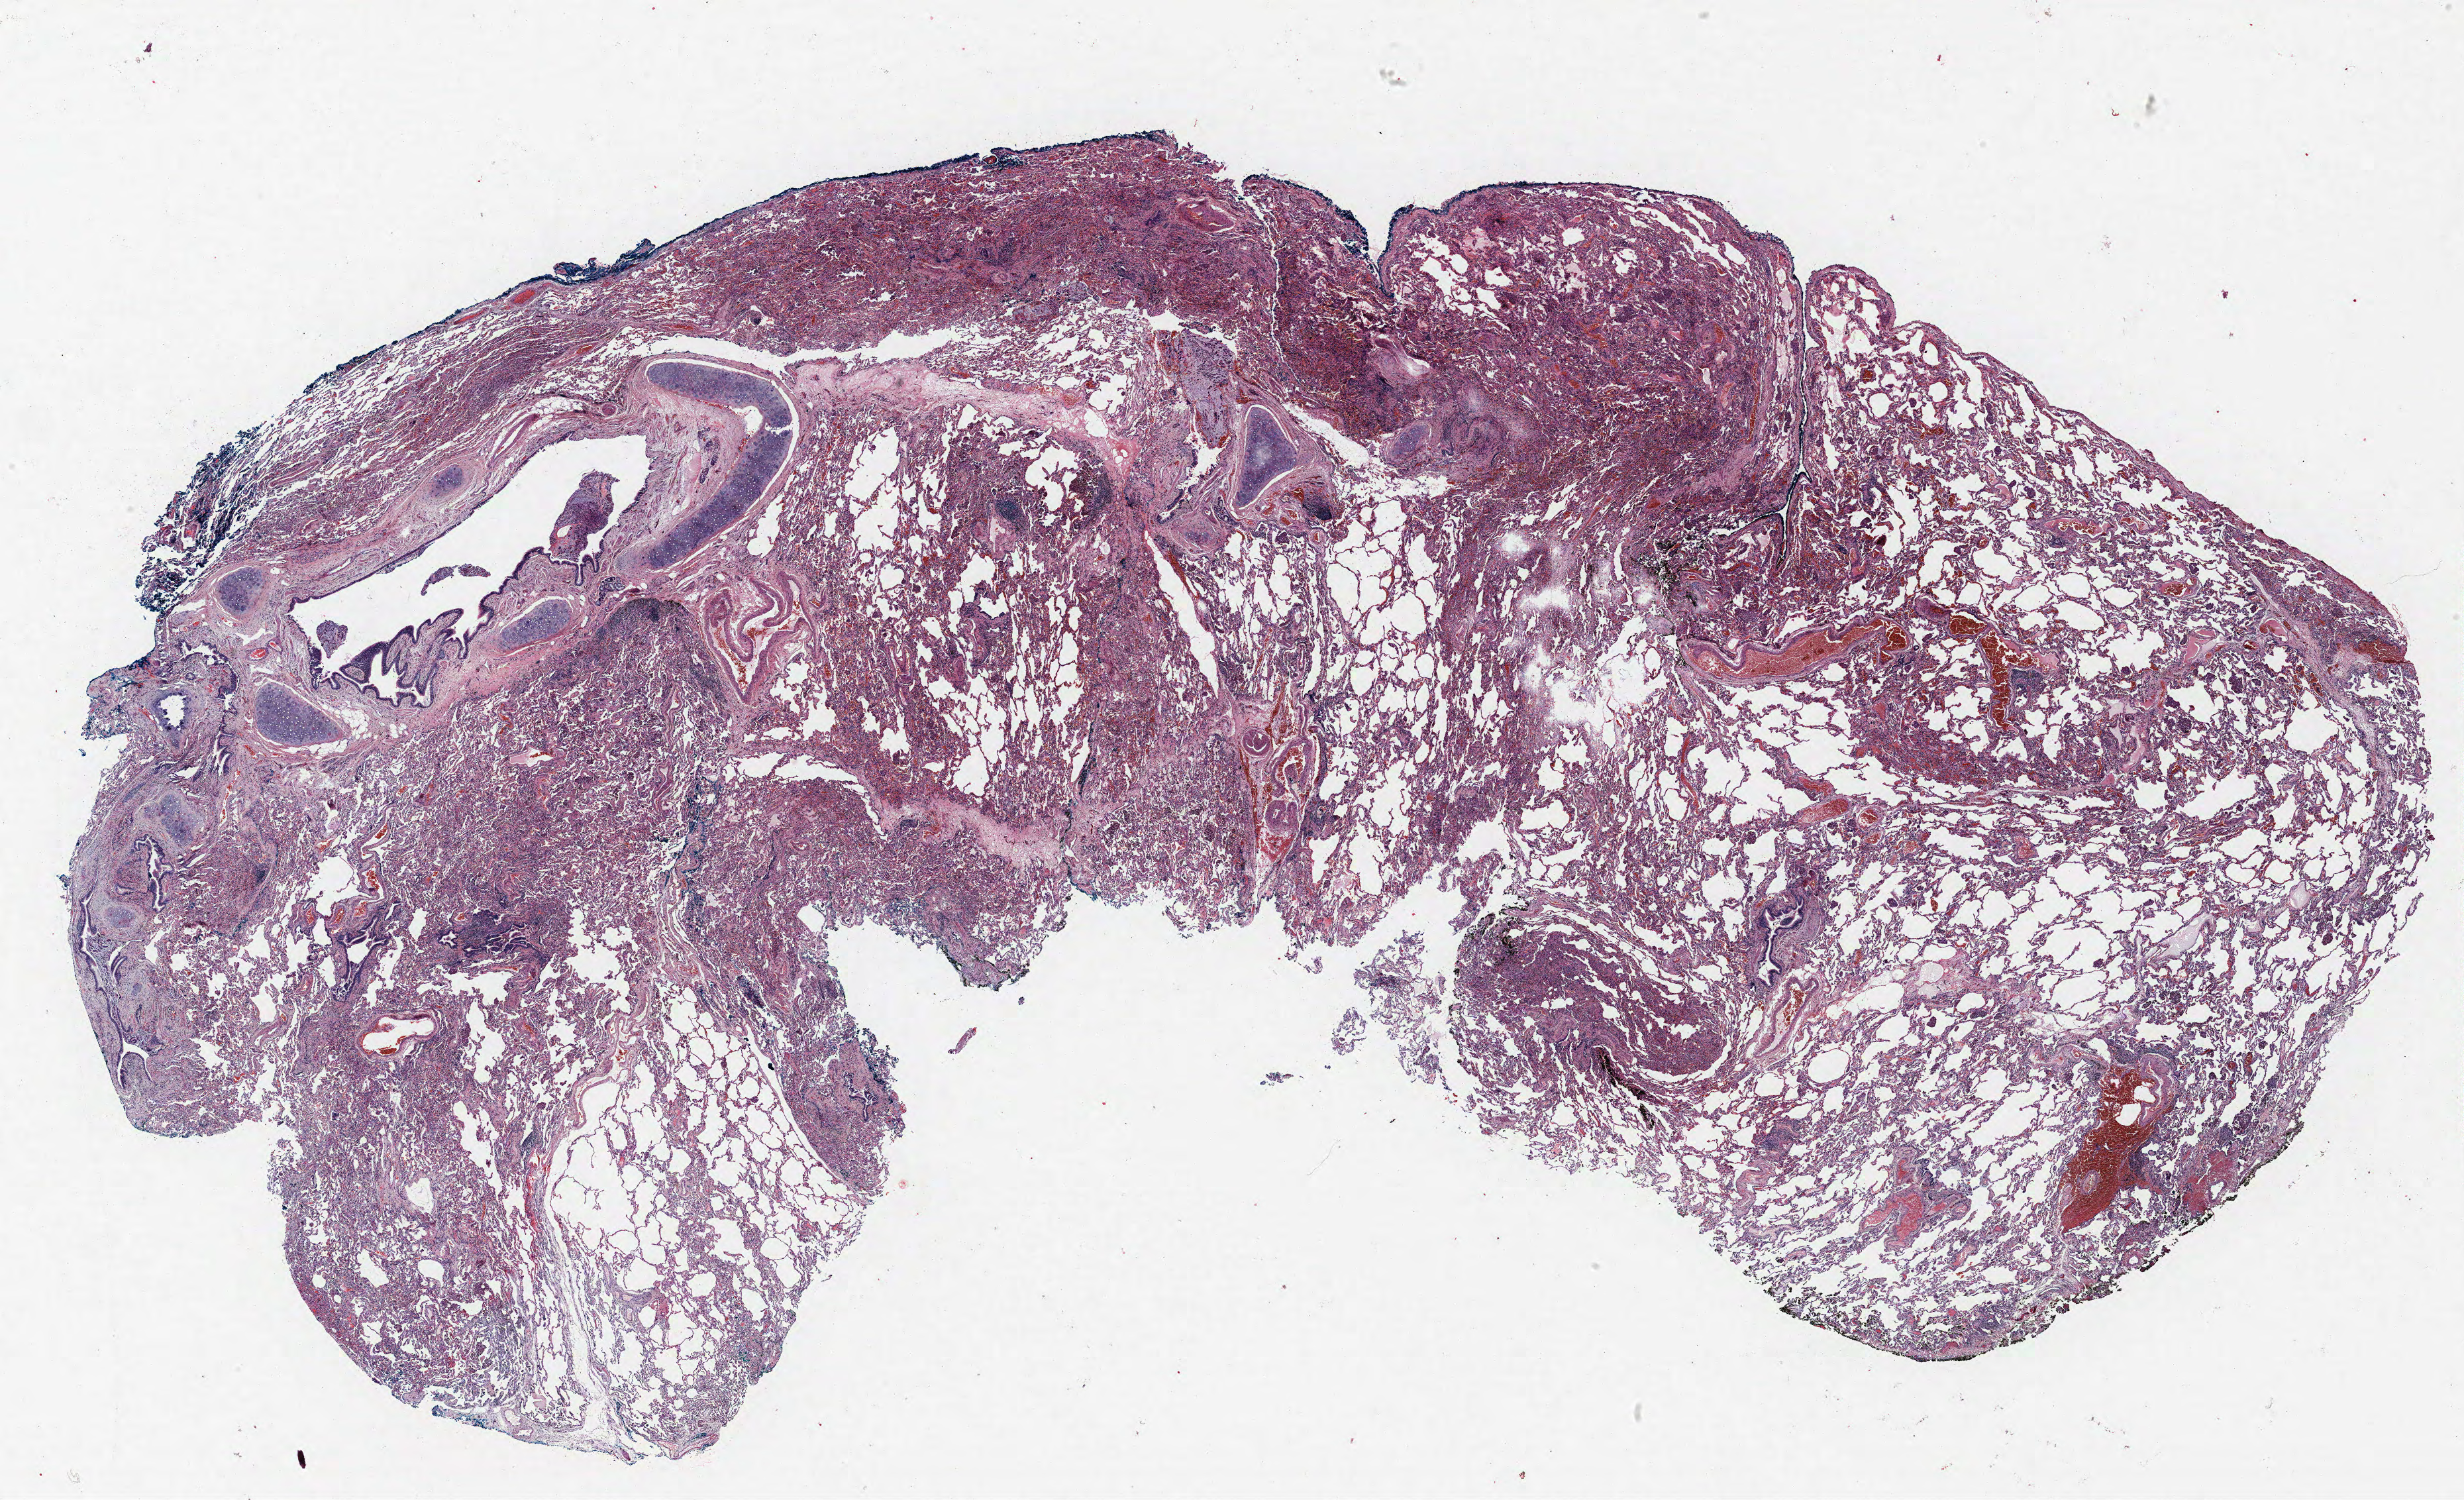
Hematoxylin and eosin (H&E) stained whole-slide image — a low-resolution overview of the entire scanned area, about 29.8 x 18.1 mm (from a 40x scan); formalin-fixed paraffin-embedded (FFPE) section; lung tissue. Male, age 60 at enrolment. Current smoker at enrolment. Grade: poorly differentiated (G3).
Primary tumour location (clinical record): left lower lobe. Tumour size (pathology): 33 mm. Participant's lung-cancer diagnosis: Large cell neuroendocrine carcinoma. Stage (AJCC 6th edition): IB. ICD-O-3 topography: lower lobe of lung (C34.3).